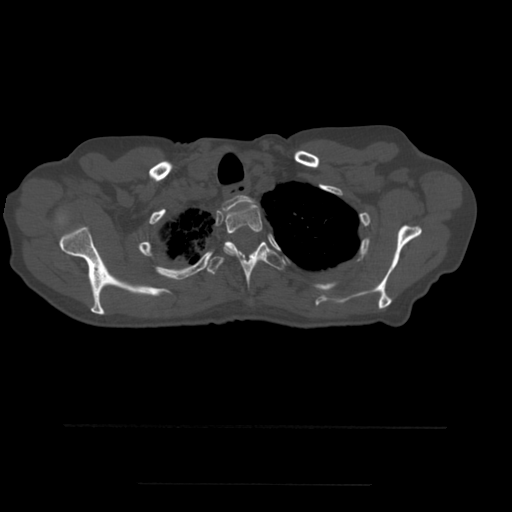
CT including the spine, one axial slice. Slice 429 of 544 in the series (ordered by position). Bone window (W 1800 / L 400 HU). 1.25 mm slice thickness. 512 × 512 image matrix, field of view 350 × 350 mm. Patient age 58 years. Case-level facts recorded for this patient, not image findings: primary cancer: lung.
Structures marked on this image (semi-automatic segmentation, software-assisted and operator-edited):
- T1 vertebra: bounding box <222,195,257,212> (left, top, right, bottom; pixels)
- T2 vertebra: <224,202,263,258>
- T3 vertebra: <207,242,286,288>